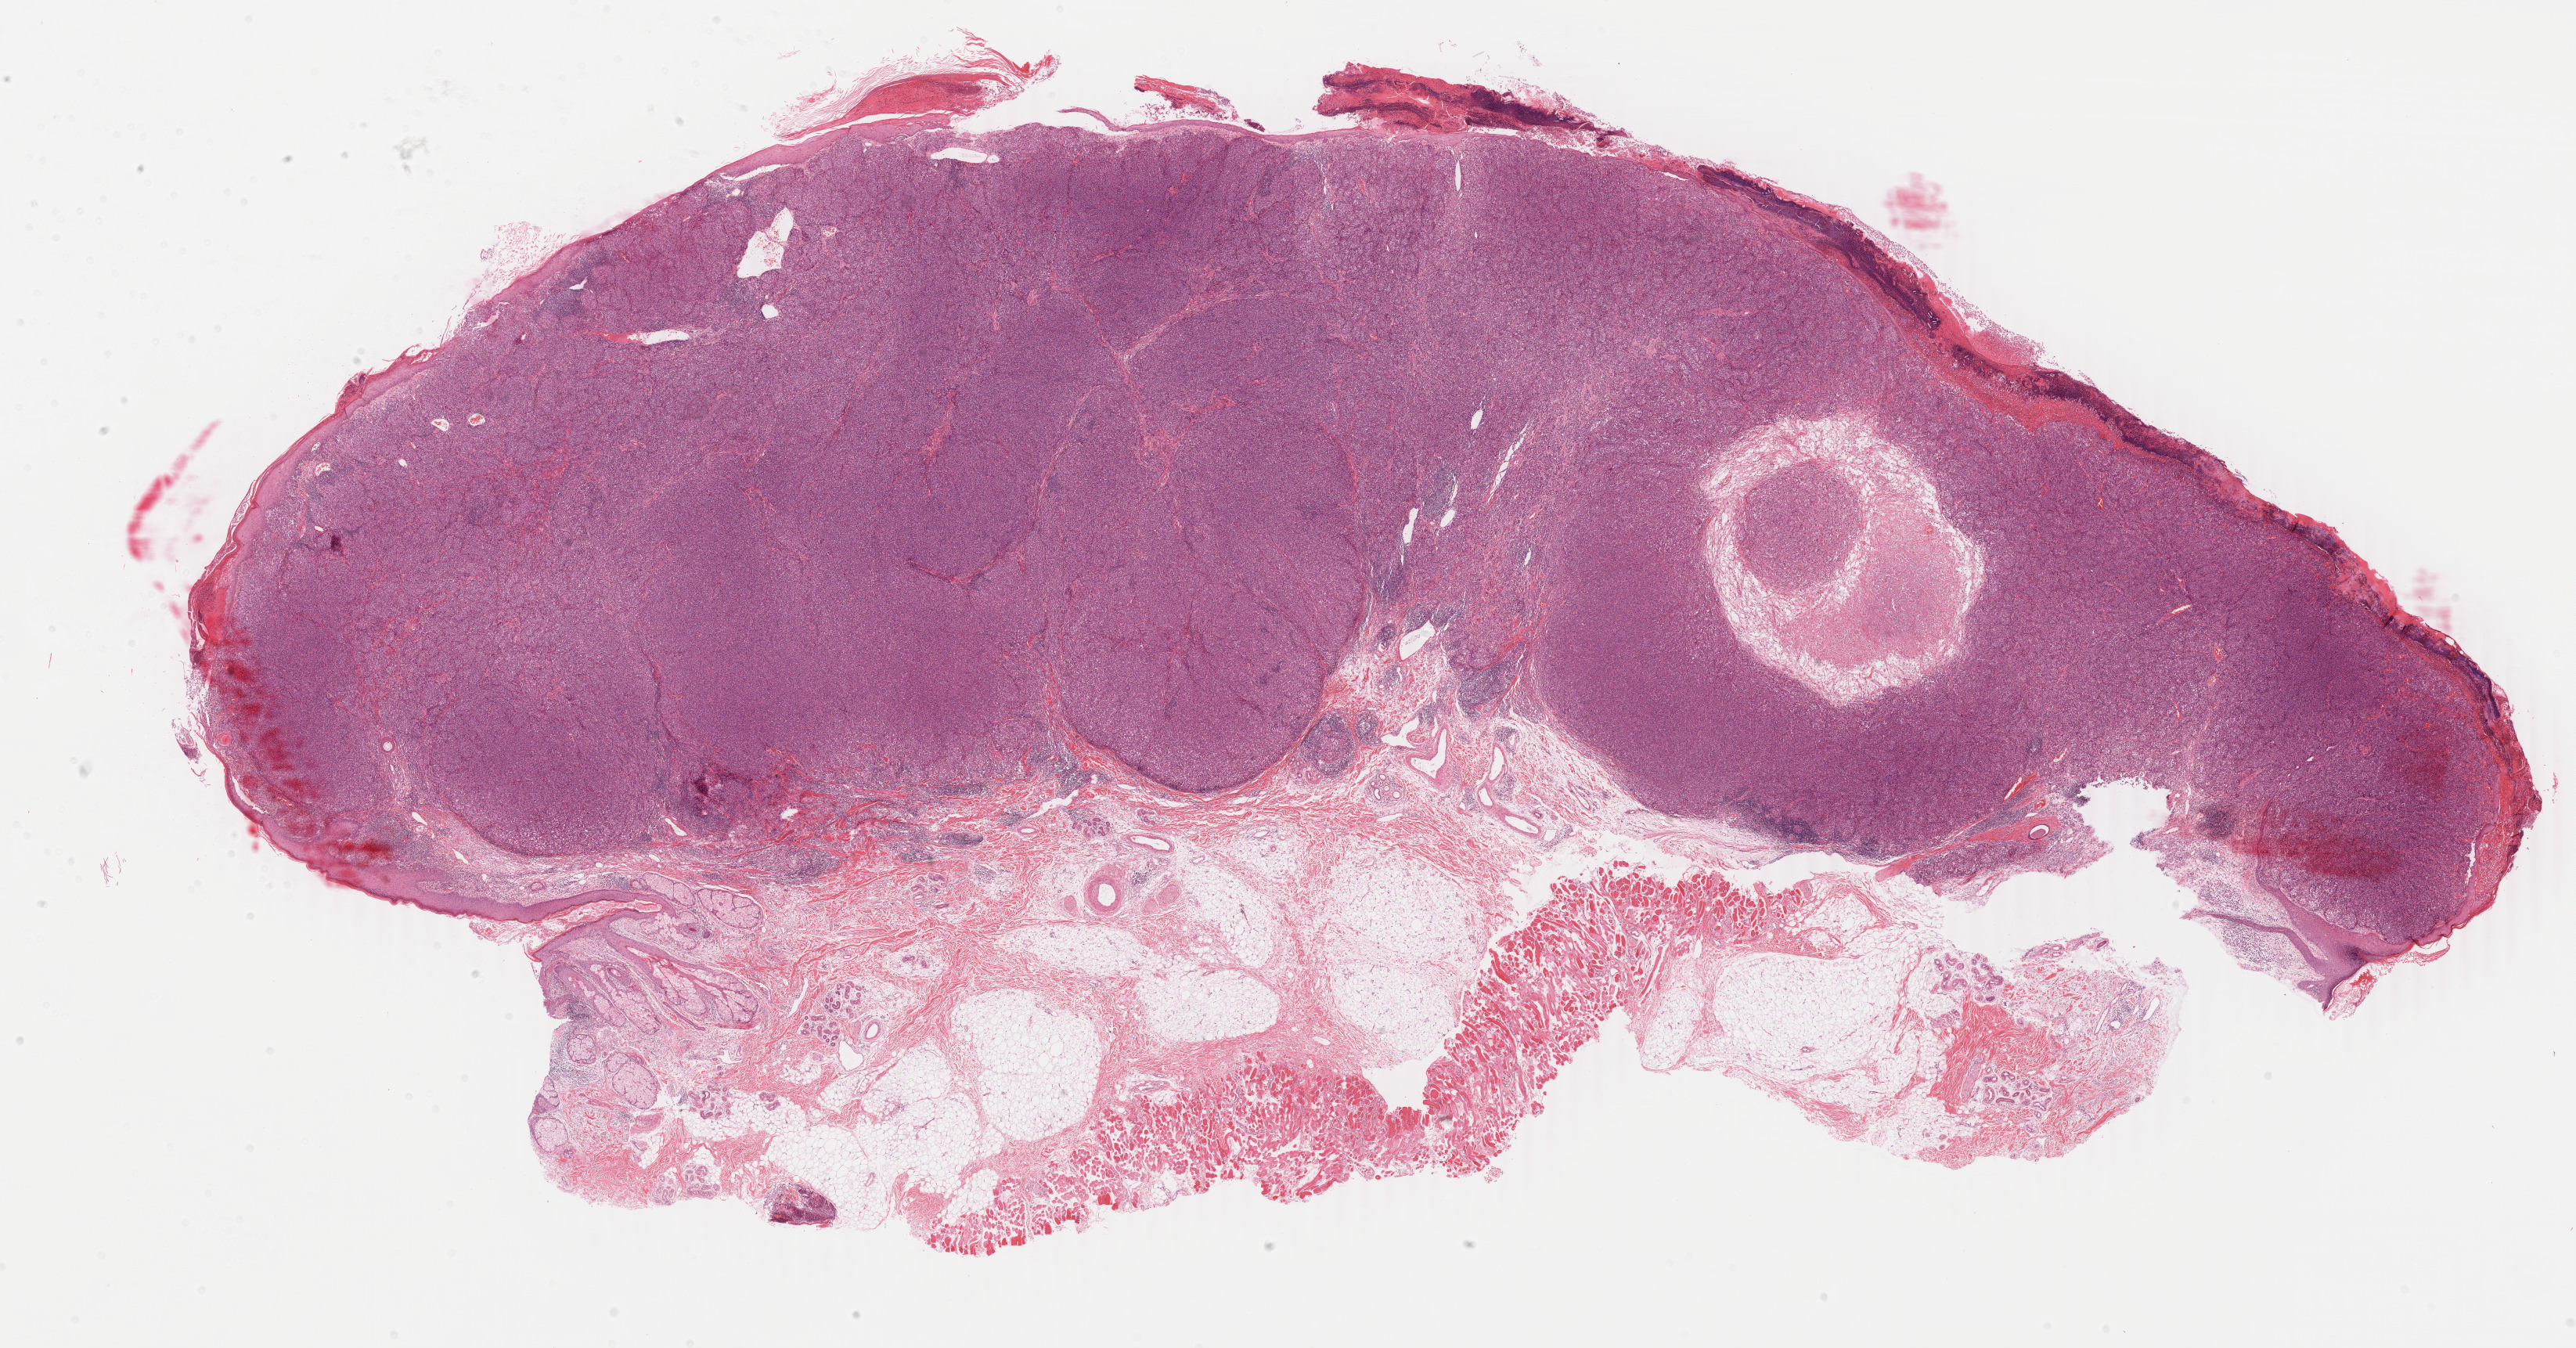
Digitized H&E tissue section (whole slide), whole scanned area (about 26.2 x 13.7 mm, from a 40x scan) shown as a low-resolution overview, formalin-fixed paraffin-embedded (FFPE) diagnostic section, primary tumour sample from the skin. Male patient.
TNM: T4b N0 M0. AJCC pathologic stage: IIC (7th edition). Pathologic diagnosis: Spindle cell melanoma, NOS.